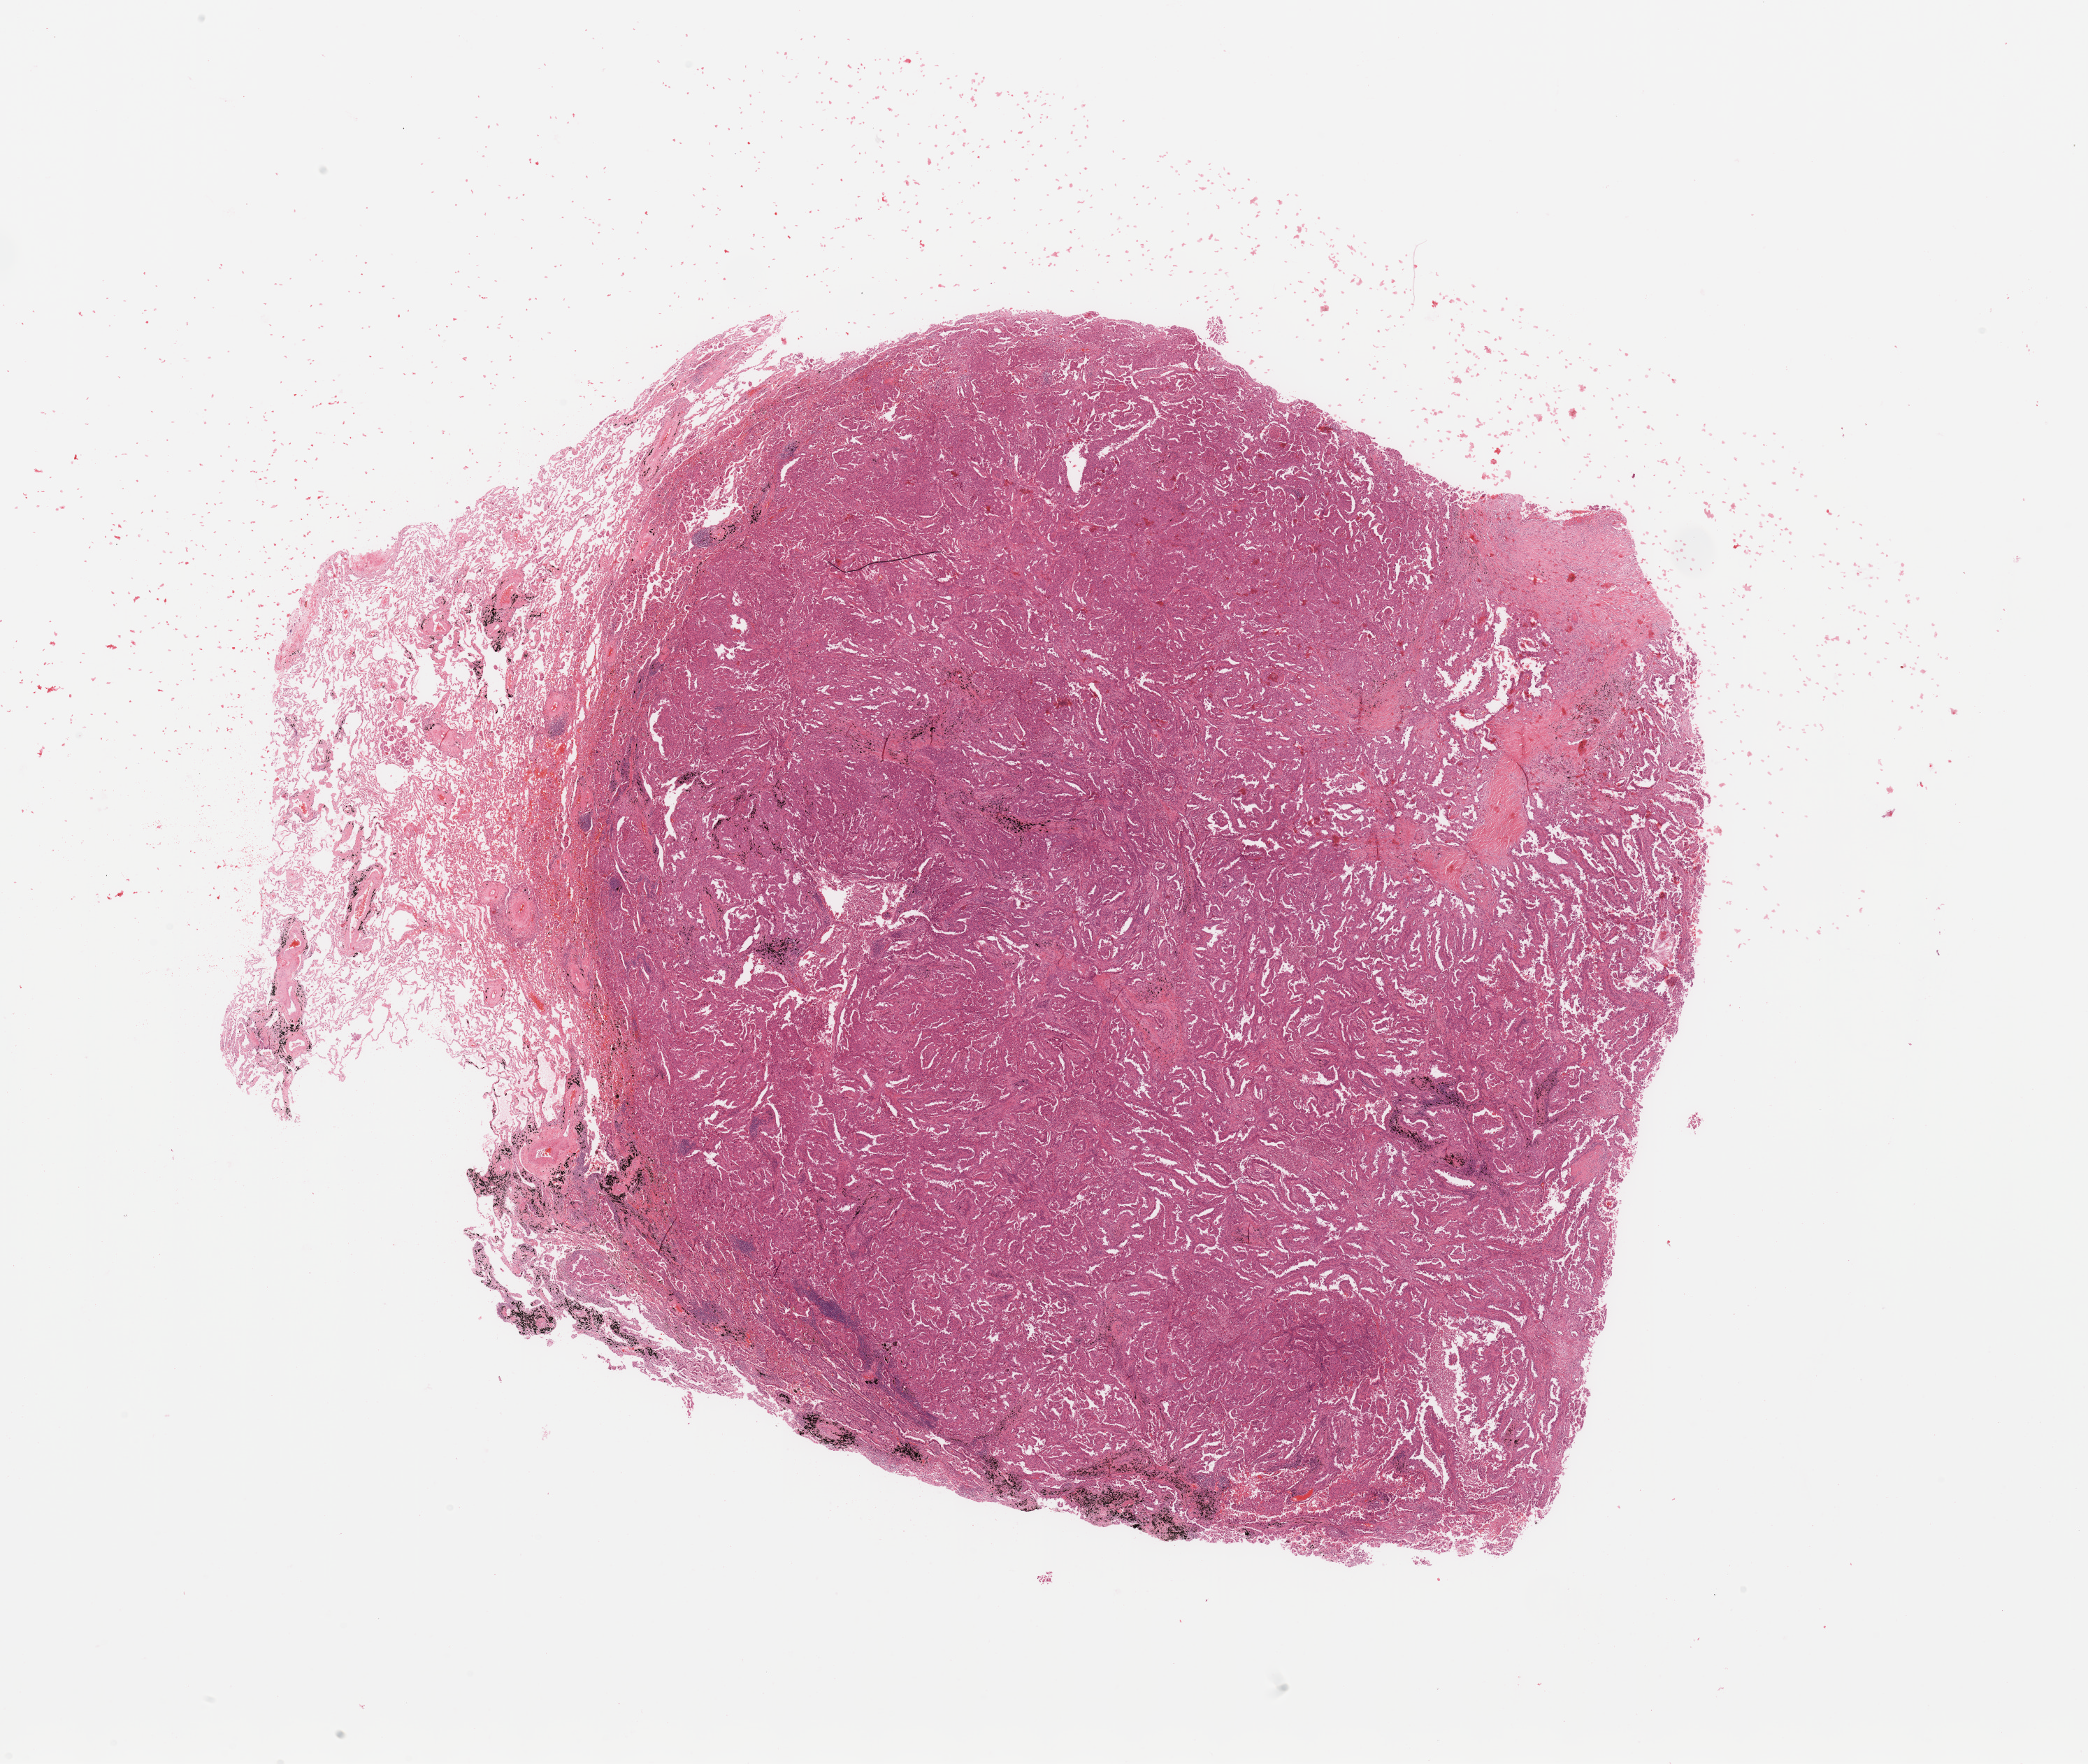
H&E-stained whole-slide image, whole scanned area (about 23.6 x 20.0 mm) shown as a low-resolution overview. Tumour tissue sample, lung. Male, 72 y/o.
Diagnosis: Adenocarcinoma, NOS.